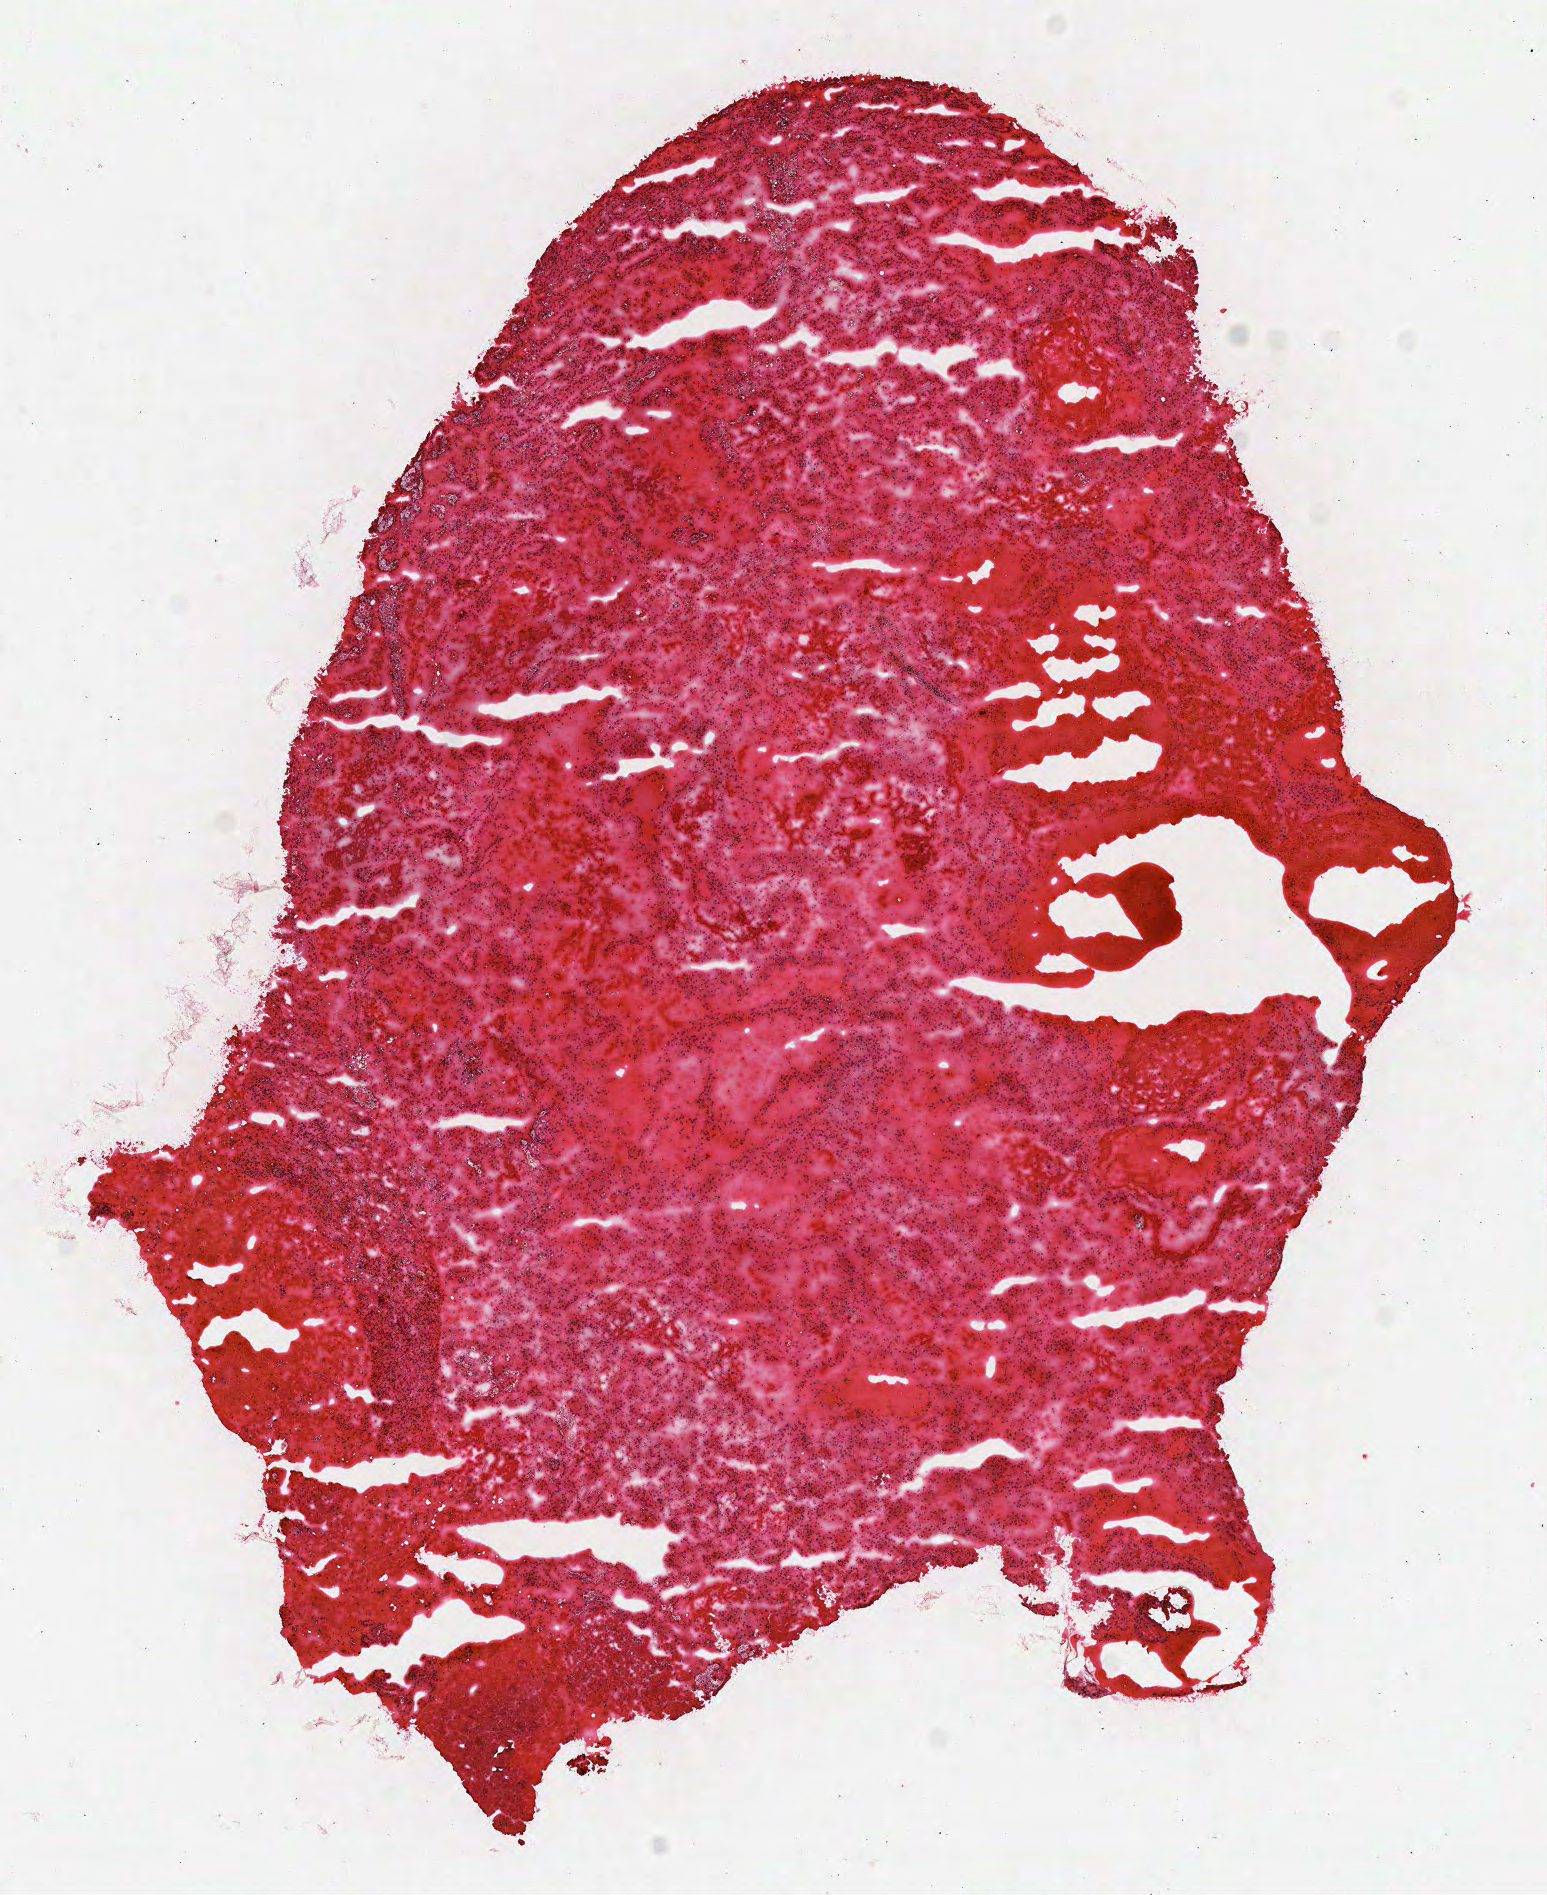
Digitized Hematoxylin and eosin (H&E) stained tissue section (whole slide), shown as a low-resolution overview of the whole scanned area (about 6.1 x 7.5 mm, from a 40x scan); frozen section; kidney, primary tumour sample. Male, age 75 years at initial diagnosis. Composition of this section per pathologist review: tumour cells 95%, tumour nuclei 85%, normal cells 0%, stromal cells 5%, necrosis 0%.
AJCC pathologic stage: III. Diagnosis: Papillary adenocarcinoma, NOS. TNM: T3a NX M0.